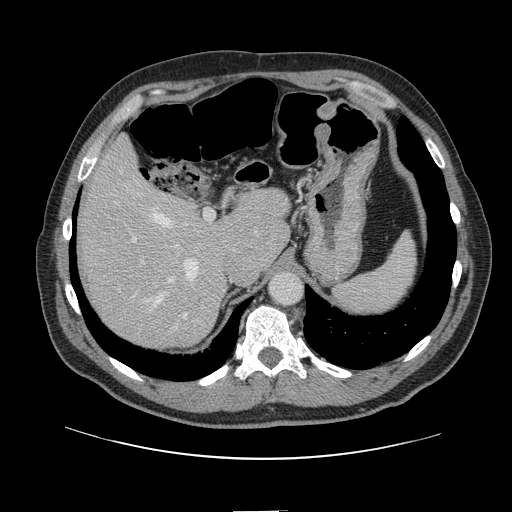
Contrast-enhanced abdominal CT, one axial slice; slice 100 of 161 in the series (ordered by position); 120 kVp; intravenous contrast given; soft-tissue window (W 400 / L 40 HU); 512 × 512 image matrix, field of view 412 × 412 mm. Male patient, age 66 years. Case-level facts recorded for this patient, not image findings: diagnosis: colorectal cancer liver metastases, imaged before liver resection; multiple liver metastases: no; largest metastasis: 3.5 cm; disease in both lobes: no.
Structures marked on this image (manually delineated by an expert):
- hepatic veins: box from (x=117, y=171) to (x=197, y=307) px
- liver: (x=81, y=143)–(x=289, y=348)
- planned liver remnant (the part of the liver to remain after resection): (x=81, y=142)–(x=289, y=307)
- portal vein (with intrahepatic branches): (x=130, y=210)–(x=216, y=308)